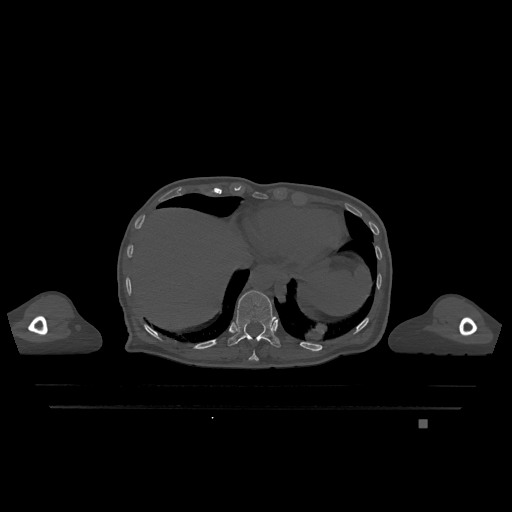
CT including the spine, one axial slice. Position 600 of 1317 along the scan axis. Bone window (W 1800 / L 400 HU). 0.5 mm slice thickness. 512 × 512 image matrix, field of view 500 × 500 mm. Patient: female, 74 years. From the clinical record (not read from this slice): primary cancer: lung; vertebrae with lytic lesions (as recorded): T1, T4, T5, T6, L4, L5.
Structures marked on this image (semi-automatically segmented with operator editing):
- T10 vertebra: bounding box (x1, y1, x2, y2) in pixels: (249, 353, 259, 361)
- T11 vertebra: (228, 290, 281, 348)